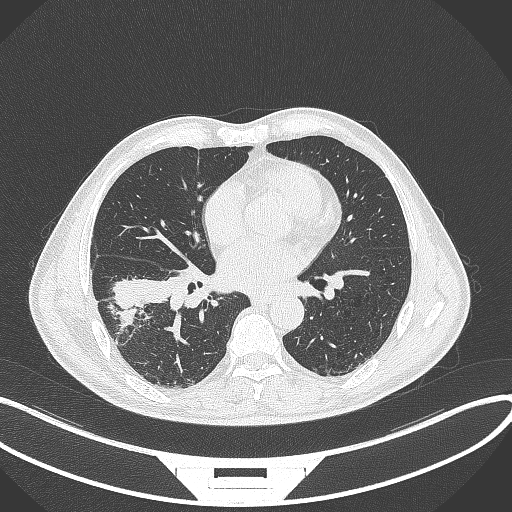
Chest CT, one axial slice. Slice 165 of 364 in the series (ordered by position). Reconstruction kernel B70f. Lung window (W 1500 / L -600 HU). 512 × 512 image matrix. Male patient, age 58 years. From the clinical record (not read from this slice): clinical TNM (as recorded): T3 N0 M0; histopathological grade: G2.
Annotated regions visible in this slice (rectangle marked by the reading radiologist):
- lung tumour (recorded histology: squamous cell carcinoma): bounding box (x1, y1, x2, y2) in pixels: (112, 275, 168, 312)